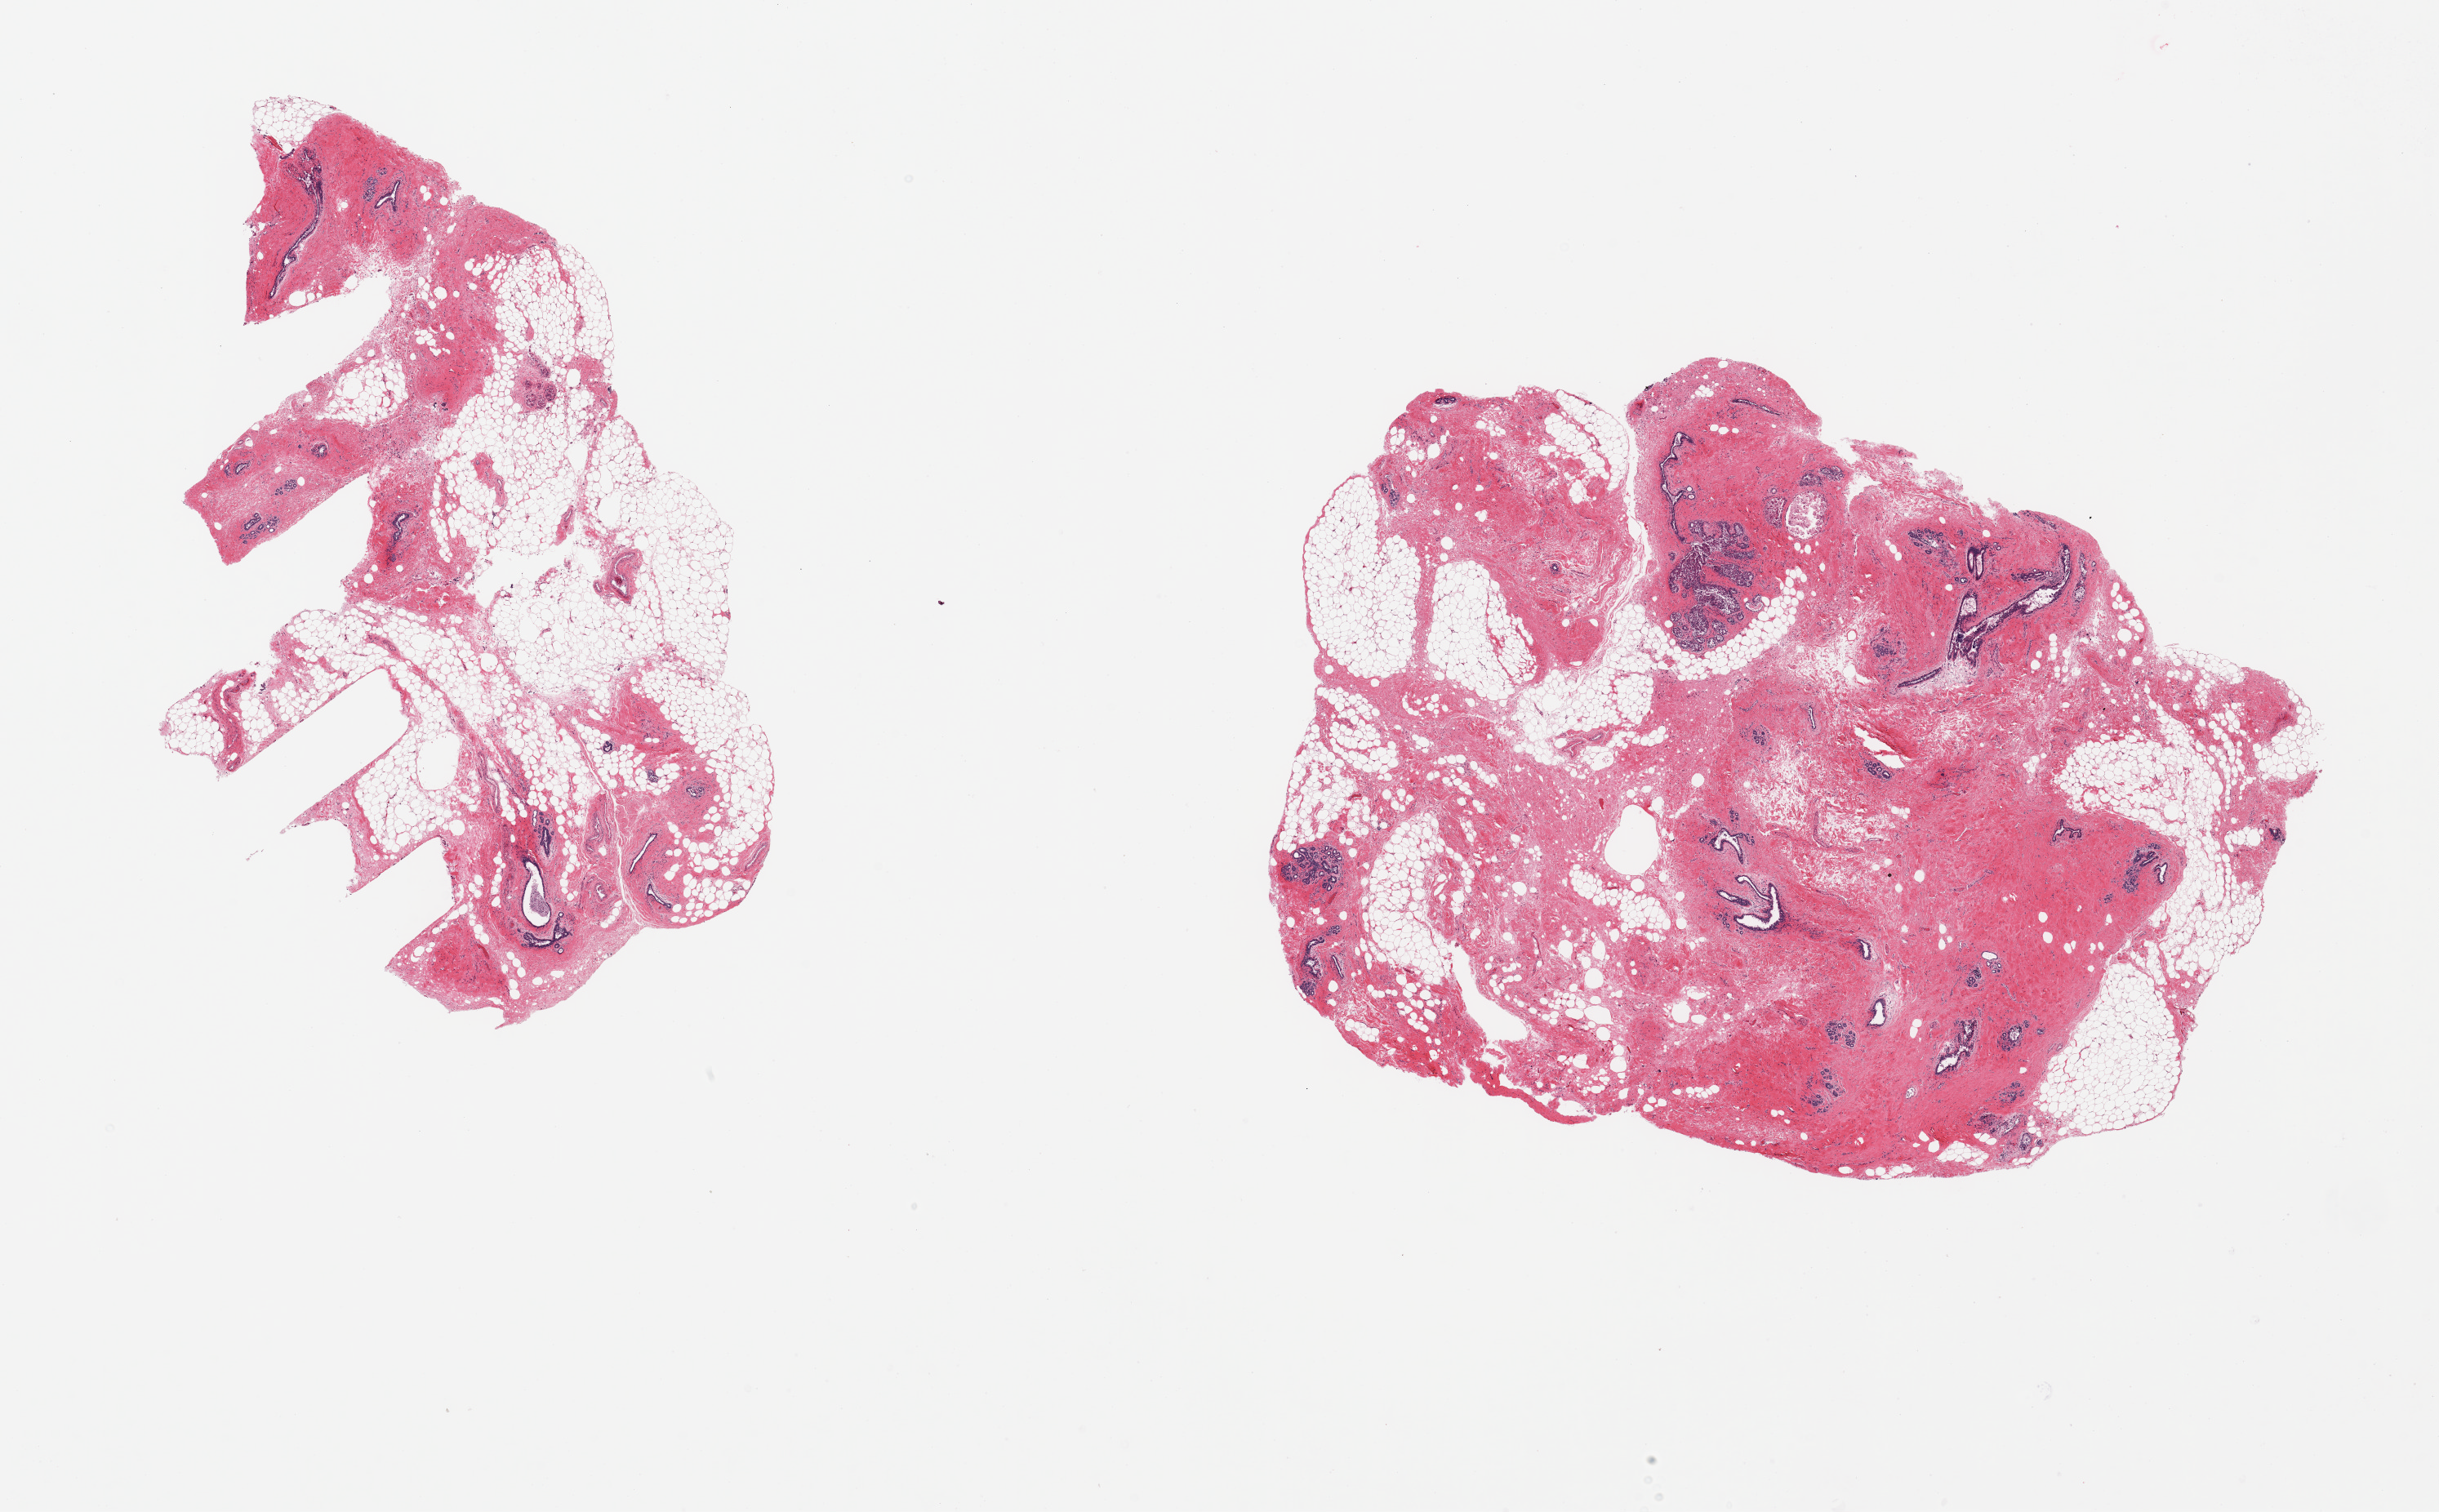
H&E whole-slide image — a low-resolution overview of the entire scanned area, about 23.6 x 14.6 mm (acquisition: 20x scan). PAXgene-fixed, paraffin-embedded tissue. Sampled site (target tissue): breast. Donor tissue sample.
Reviewer comment on this tissue sample: 2 pieces; ductal & lobular tissue; foci of intraductal hyperplasia.